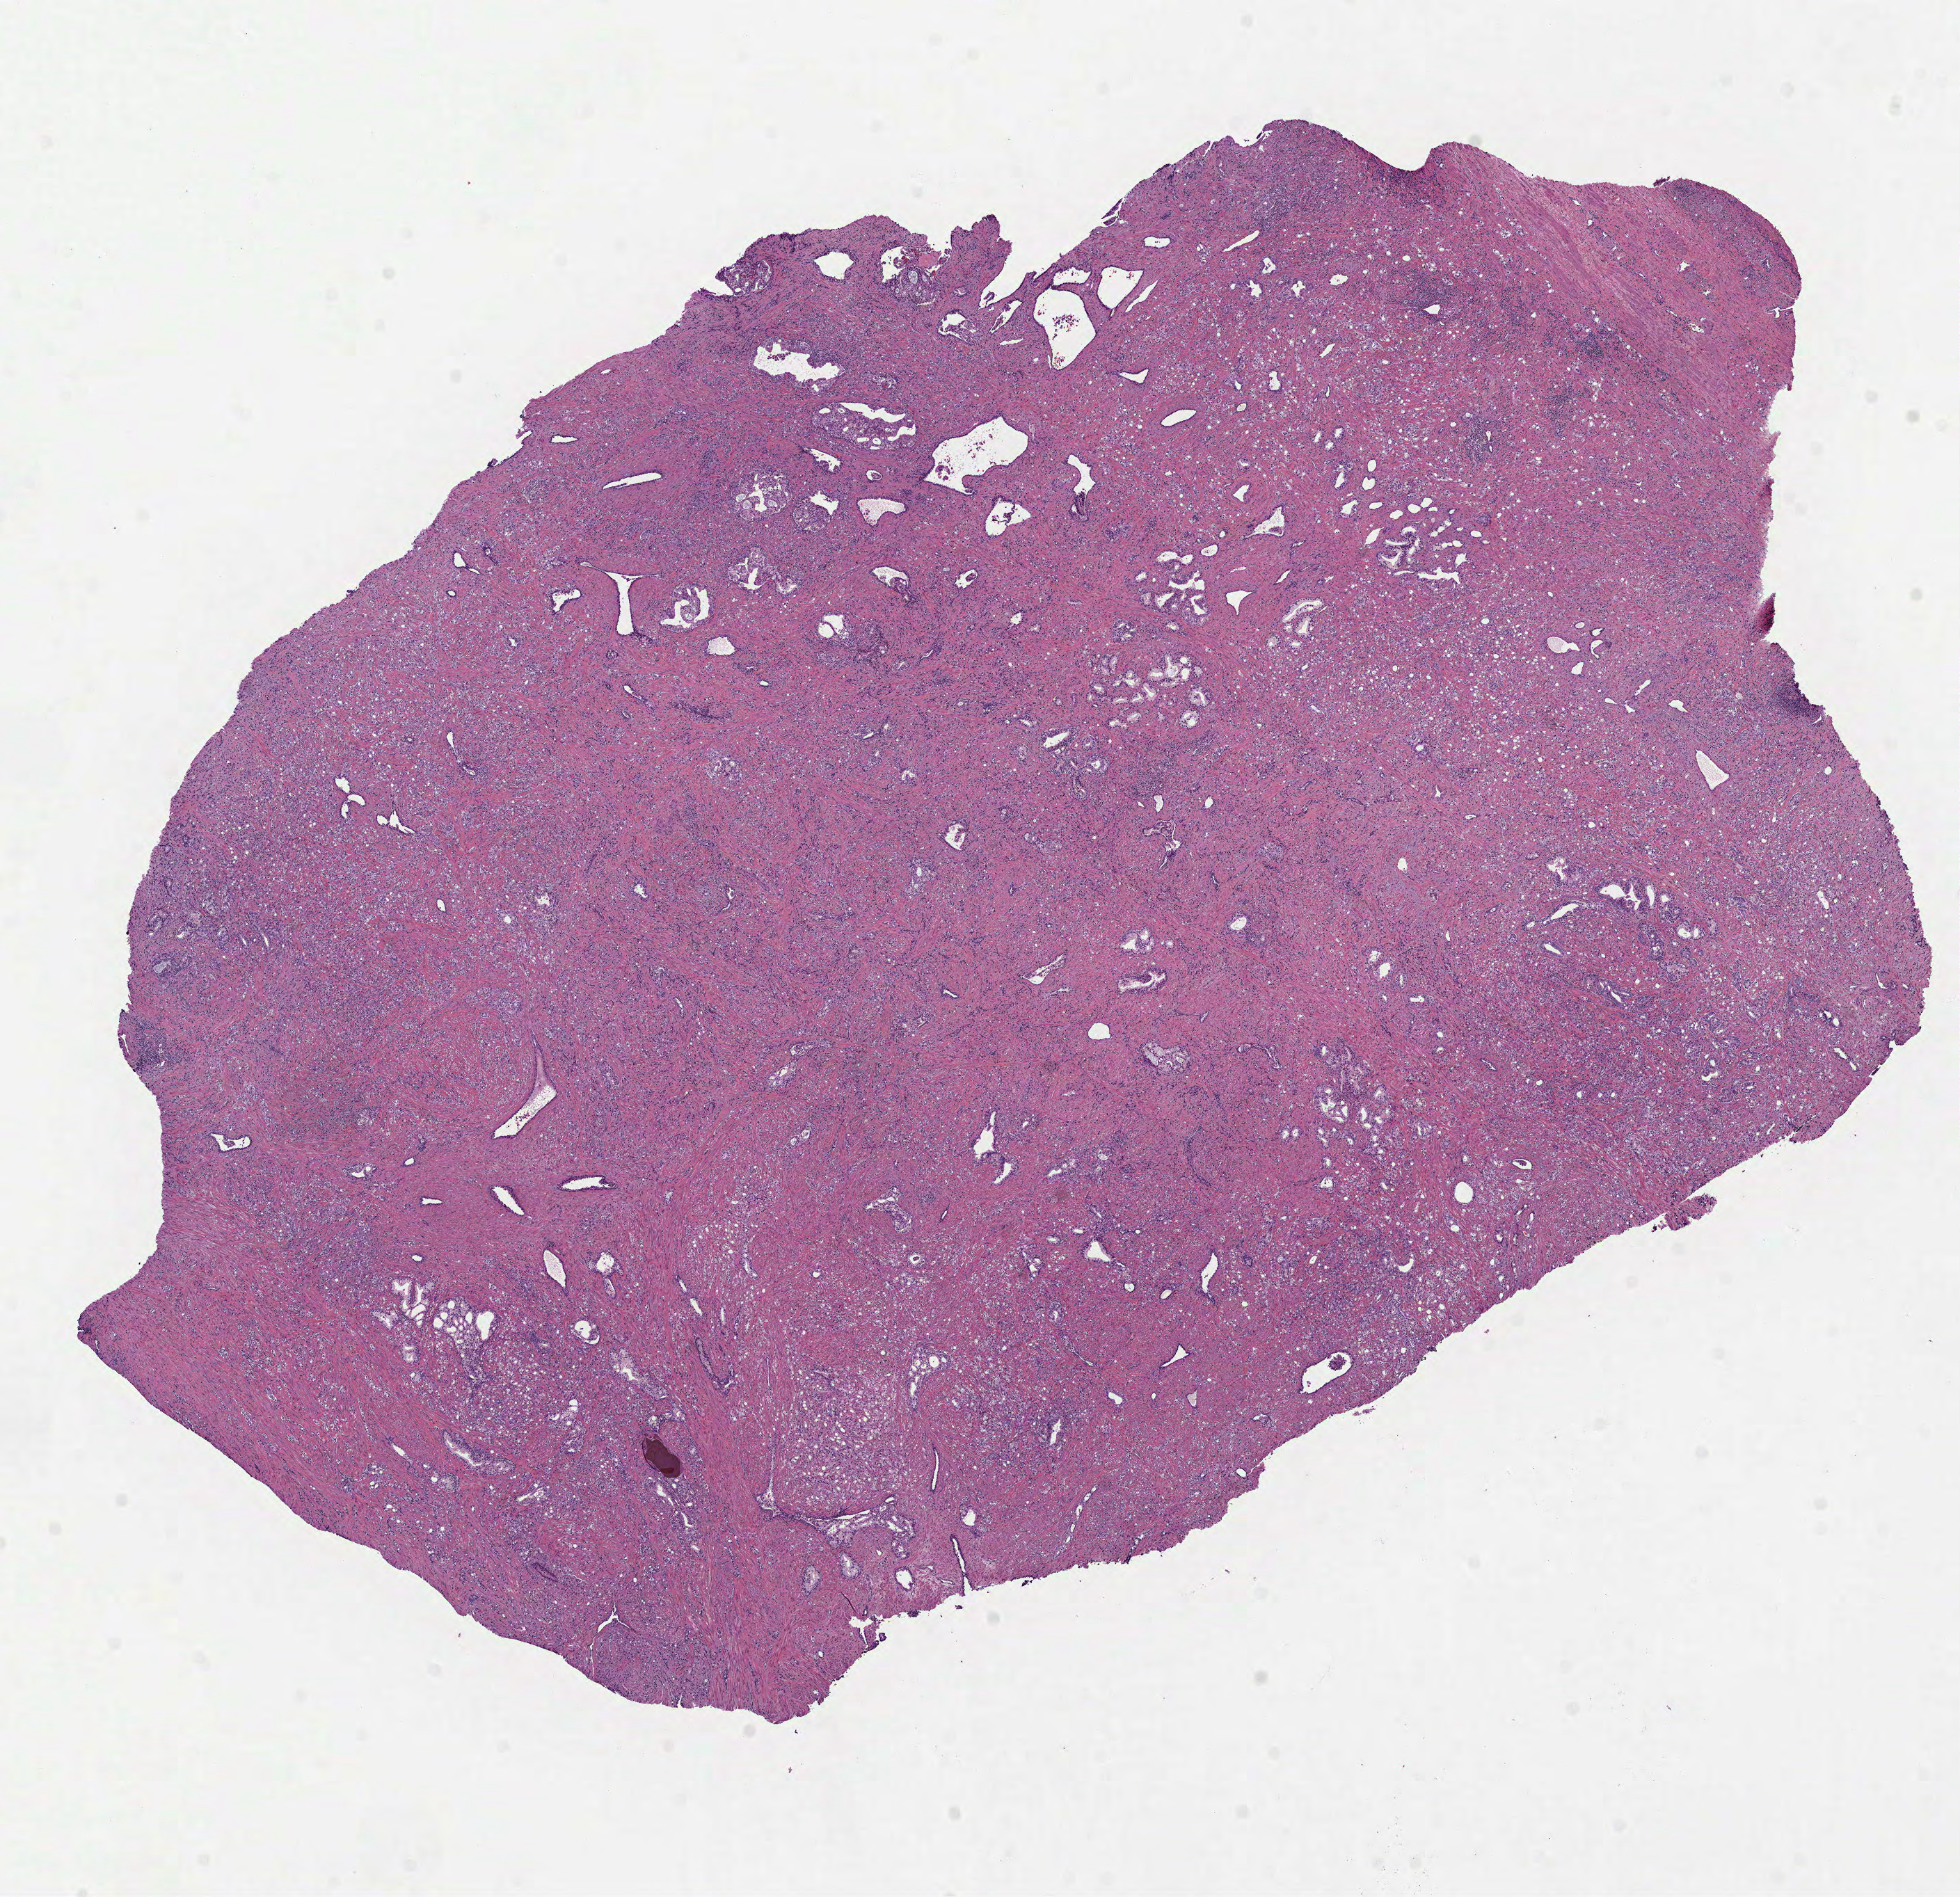
Whole-slide histology image, H&E-stained — low-resolution overview of the scanned area, about 11.4 x 11.0 mm (slide scanned at 40x); formalin-fixed paraffin-embedded (FFPE) diagnostic section; prostate, primary tumour sample. Patient: male, age at initial diagnosis 54 years. Gleason score: 8 (4+4).
• lymph nodes positive (case pathology): 2 of 7 examined
• diagnosis: Acinar cell carcinoma
• laterality: bilateral